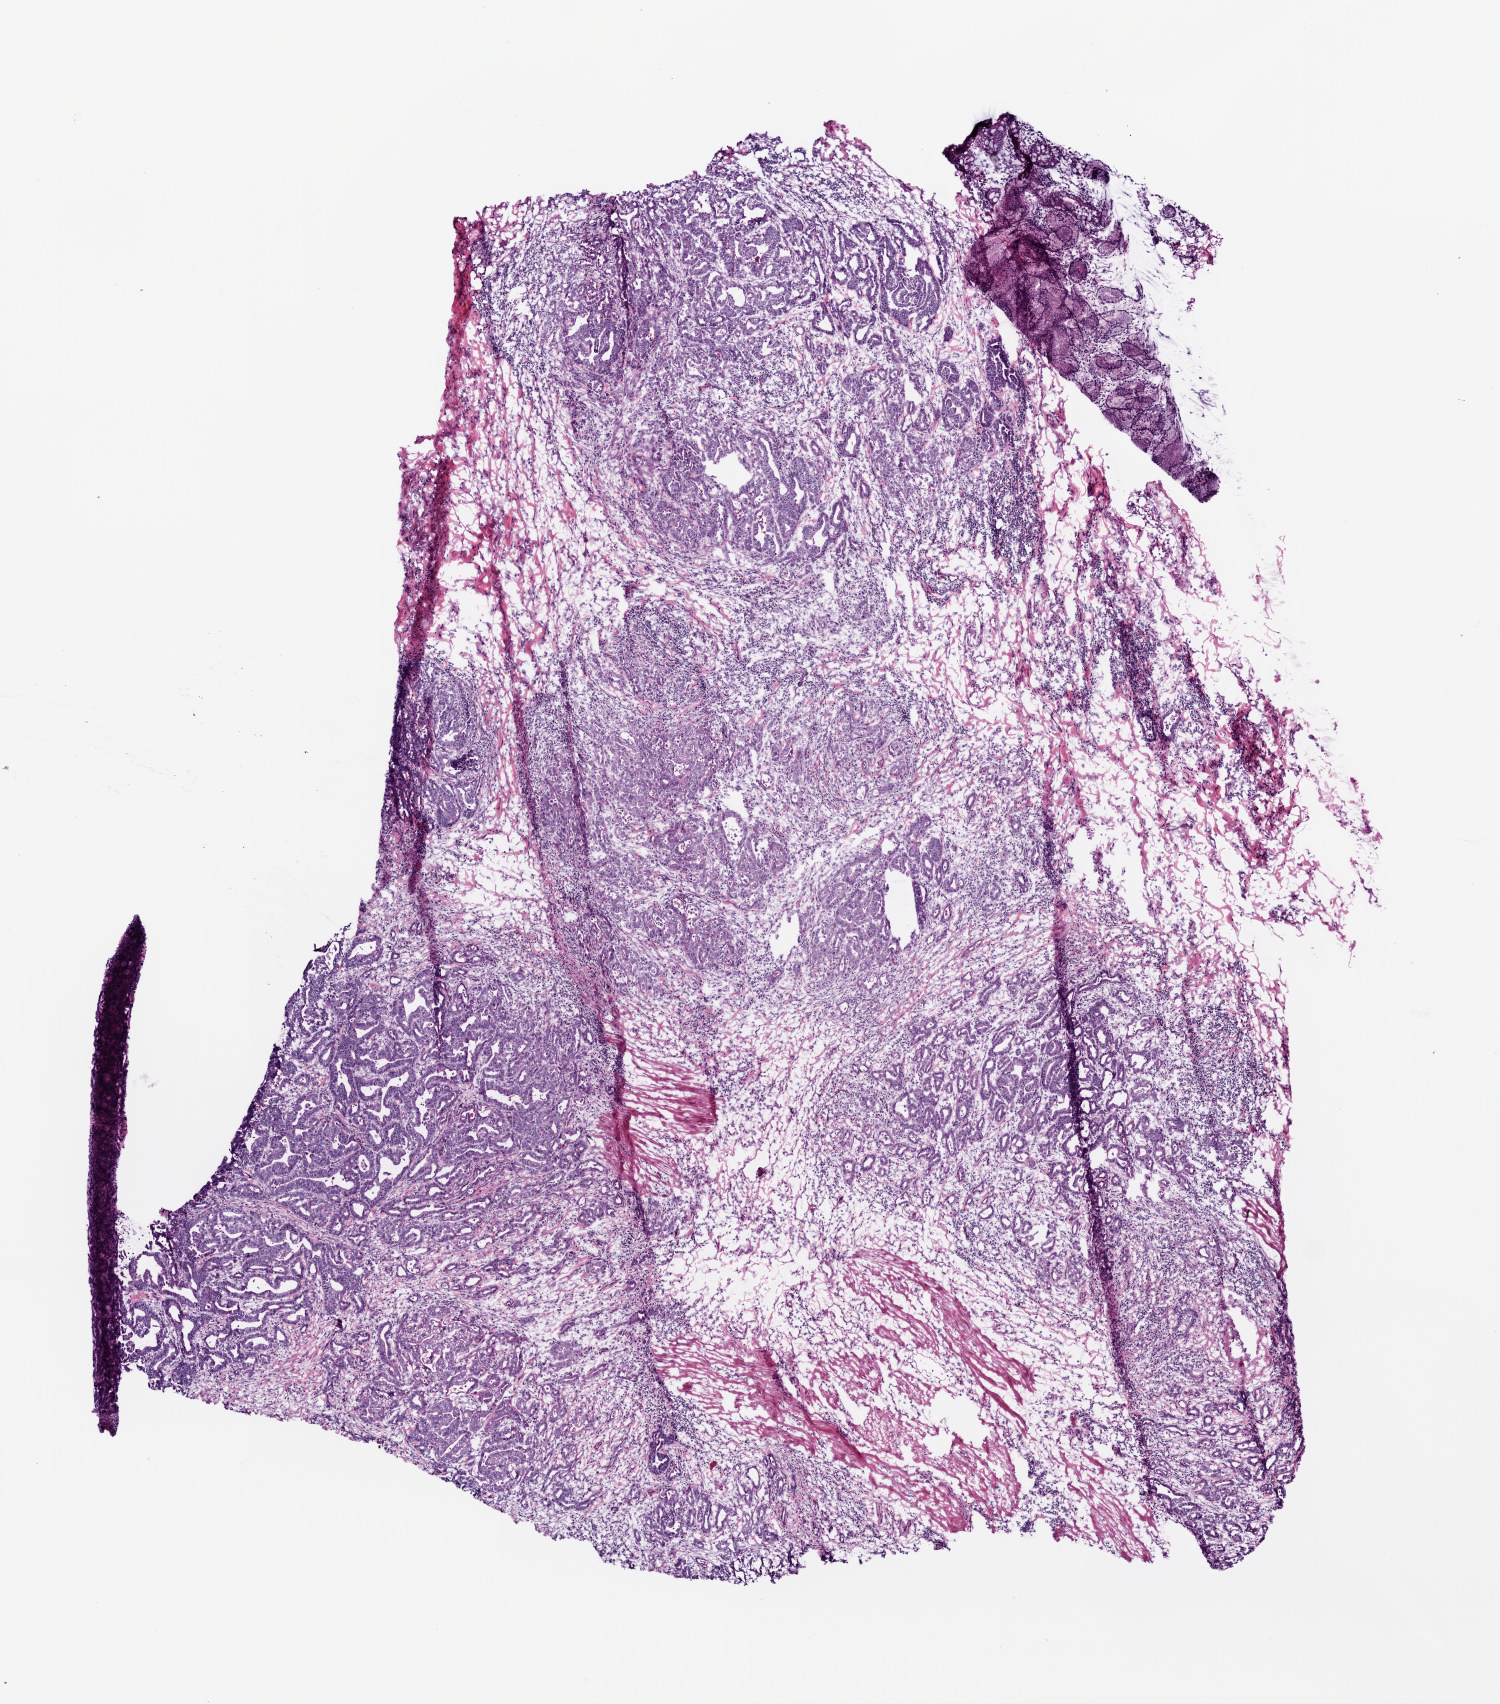
Digitized H&E tissue section (whole slide), a low-resolution overview of the entire scanned area, about 6.0 x 6.8 mm (slide scanned at 20x). Frozen section. Stomach, primary tumour sample. Male patient; age at initial diagnosis 69 years. Histologic grade: G3 (poorly differentiated). Composition of this section per pathologist review: tumour cells 72%, tumour nuclei 70%, normal cells 3%, stromal cells 25%, necrosis 0%. Inflammatory infiltration, as recorded: lymphocyte infiltration 20%, monocyte infiltration 0%, neutrophil infiltration 8%.
Diagnosis: Adenocarcinoma, NOS (gastric antrum). Lymph nodes positive (case pathology): 2 of 41 examined. AJCC pathologic stage: II (6th edition).